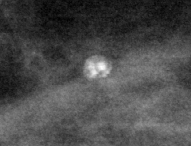
Crop from a digitized film mammogram around one marked abnormality, right breast, MLO view, BI-RADS breast density category 1 (scale 1–4).
- Marked abnormality: mass, shape lymph node, margins circumscribed; BI-RADS assessment category 2; subtlety rating 4 on a 1 (subtle) to 5 (obvious) scale; benign without callback (not worked up further).